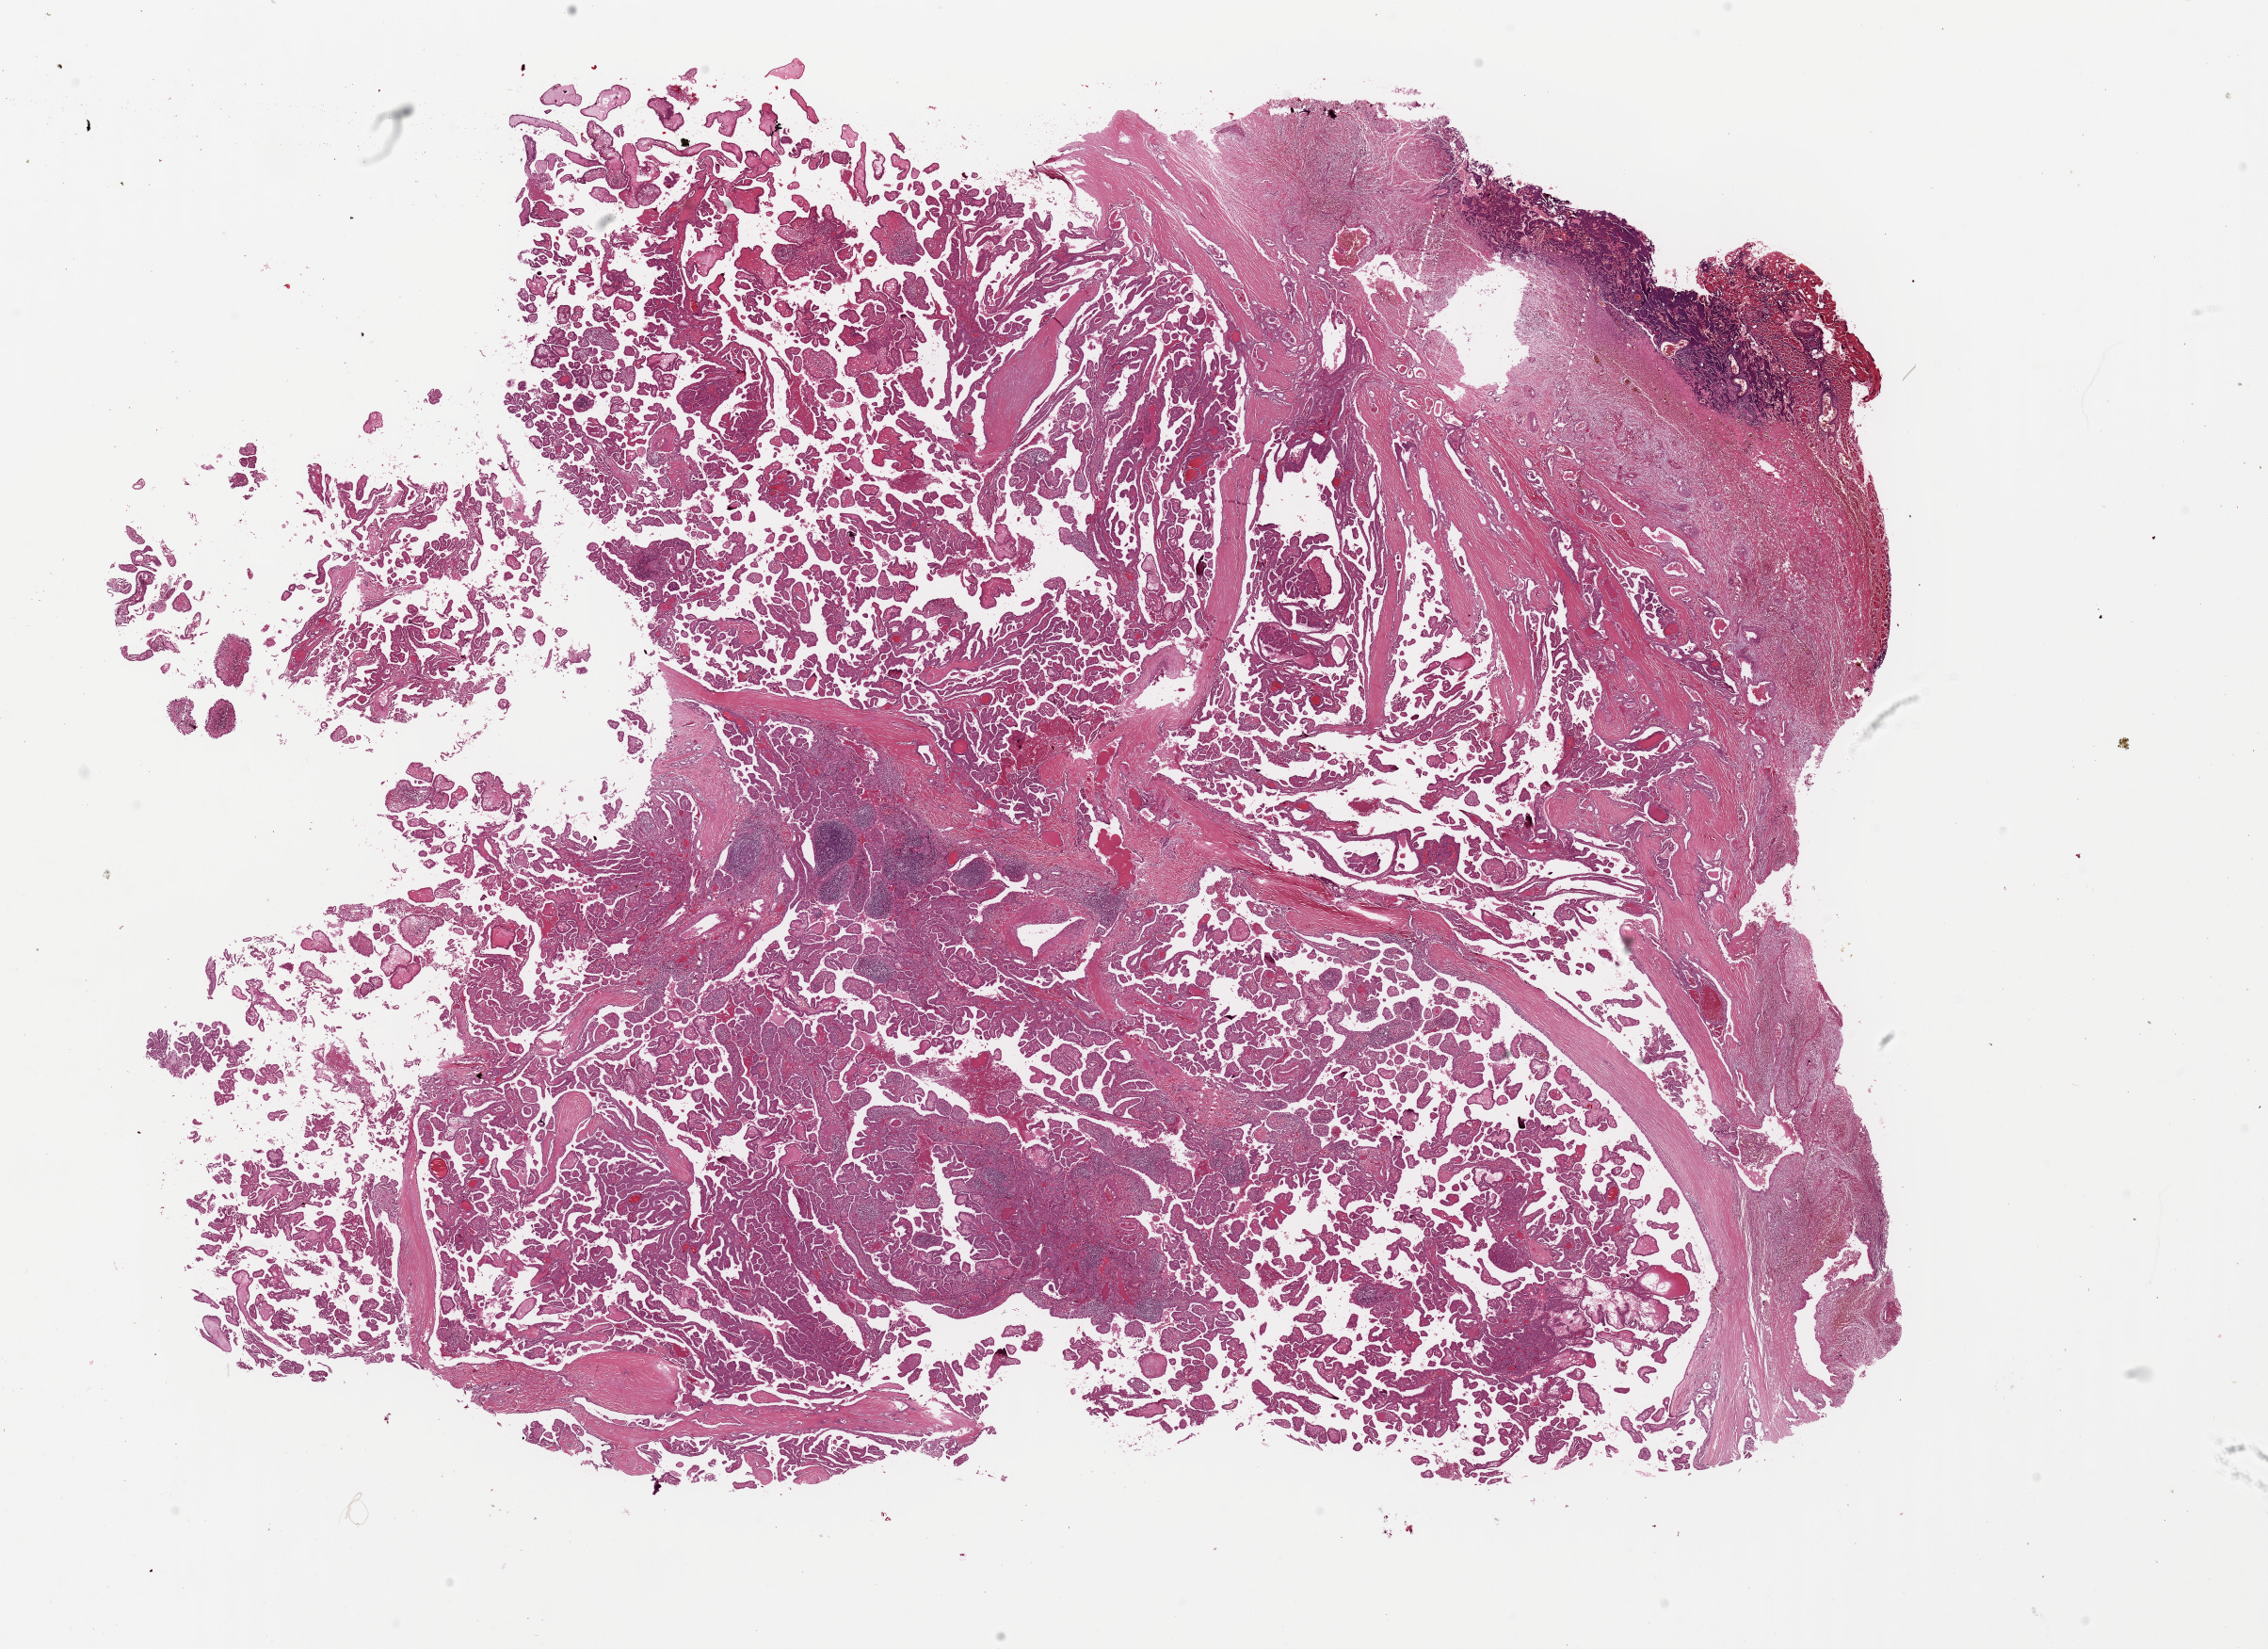
Whole-slide histology image, H&E — low-resolution overview of the scanned area, about 19.0 x 13.8 mm (from a 40x scan); formalin-fixed paraffin-embedded (FFPE) diagnostic section; thyroid, primary tumour sample. Patient: female, age at initial diagnosis 51 years.
Pathologic diagnosis: Papillary adenocarcinoma, NOS (thyroid gland).